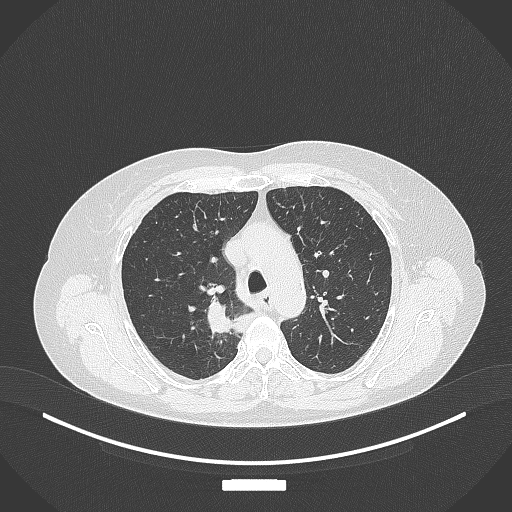
Chest CT, one axial slice; slice 277 of 357 in the series (ordered by position); reconstruction kernel B70f; lung window (W 1500 / L -600 HU); 512 × 512 image matrix, field of view 400 × 400 mm. Female patient, age 62 years. From the clinical record (not read from this slice): clinical TNM (as recorded): T1c N1 M0.
Outlined on this slice (bounding box drawn by a radiologist):
- lung tumour (recorded histology: squamous cell carcinoma): box from (x=201, y=289) to (x=239, y=346) px